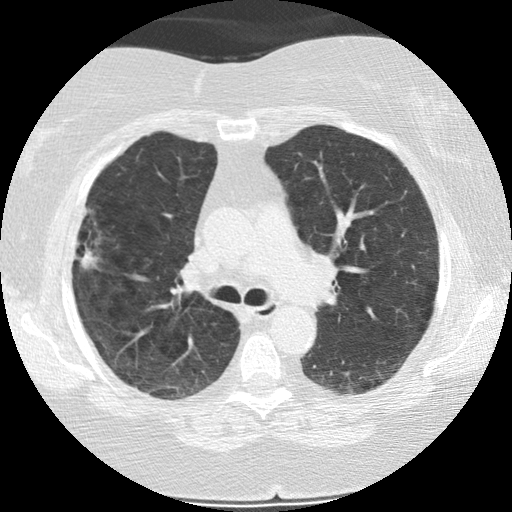
Chest CT (low-dose screening protocol), one axial image; baseline annual screen; lung window (W 1500 / L -600 HU); 120 kVp; slice 71 of 187 in the series. Female participant, aged 73 years at enrolment.
Lesion marked by an expert reader, bounding box (x1, y1, x2, y2) in pixels: (60, 210, 110, 275). Screening reader's record for this exam (one nodule recorded; not confirmed to be the boxed lesion): non-calcified nodule or mass ≥4 mm, right upper lobe, 21 × 14 mm, poorly defined margins, soft tissue attenuation. Participant outcome: lung cancer diagnosed 482 days after this screen (after the second annual screen) — bronchiolo-alveolar adenocarcinoma, NOS, right upper lobe, moderately differentiated (G2), stage IIIB (AJCC 6th edition), 21 mm at pathology.